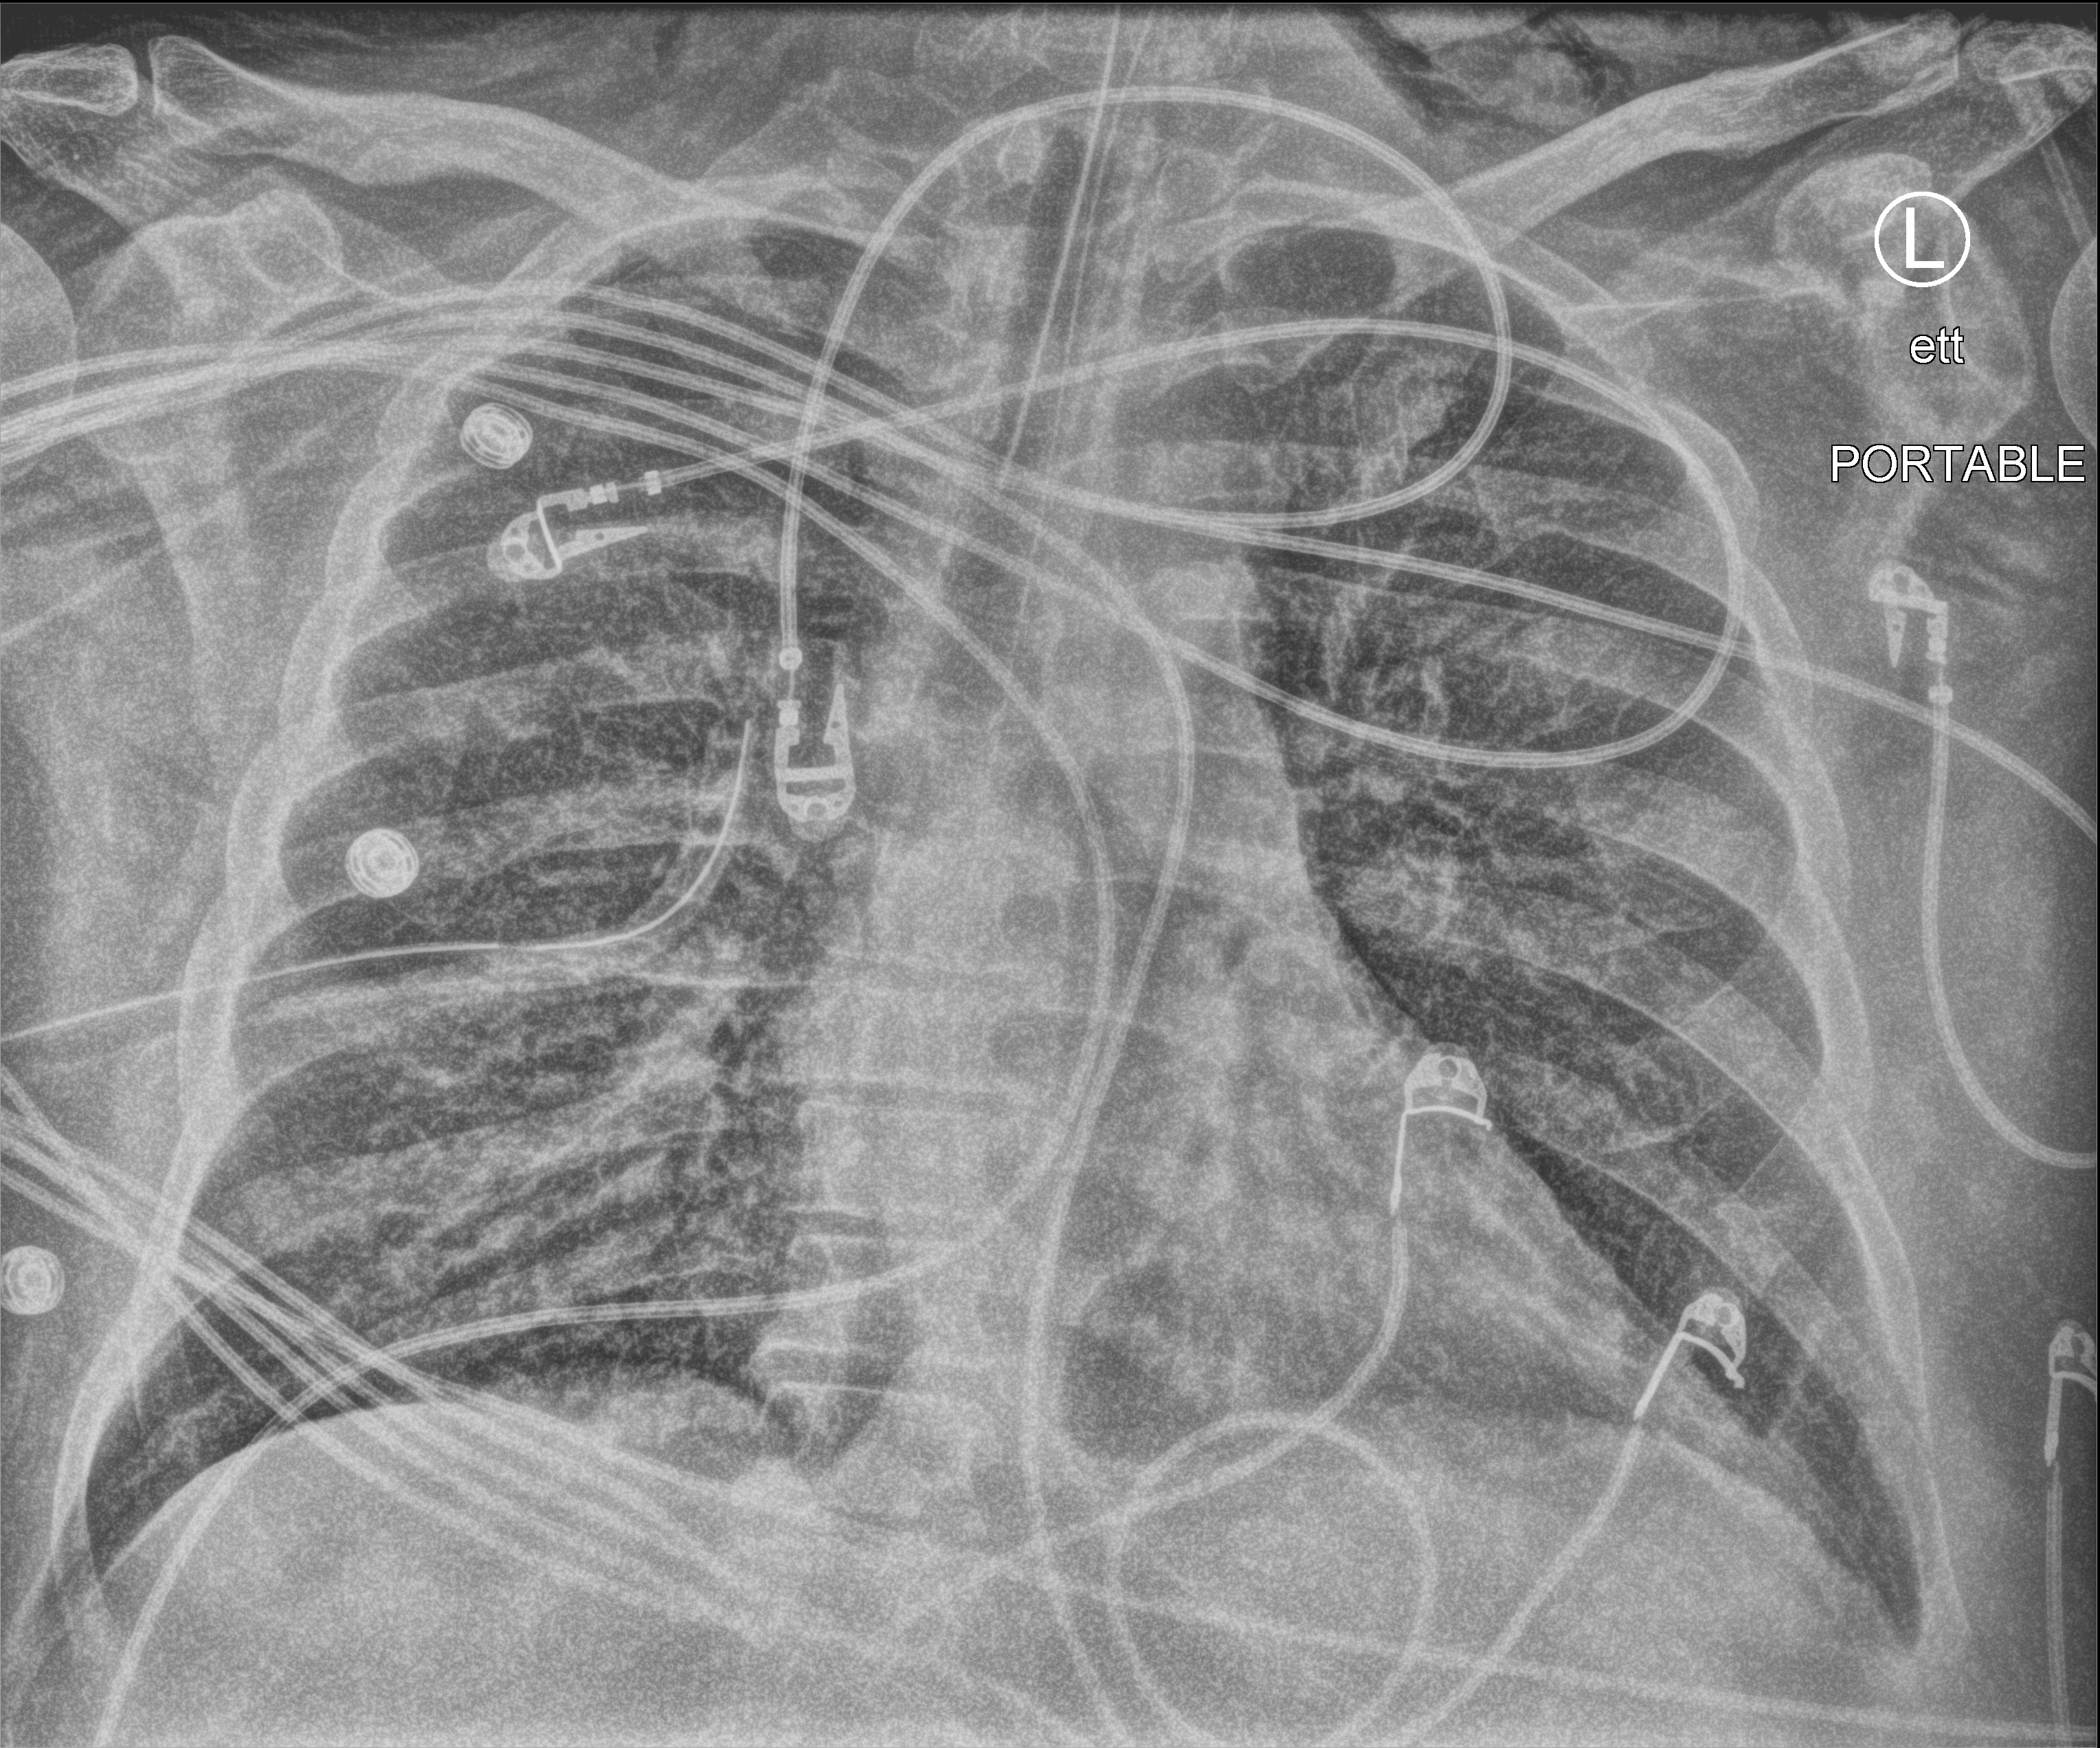
Bedside chest radiograph (computed radiography); anteroposterior (AP) projection. Patient hospitalised with COVID-19, aged 18–59 years.
Hospital-stay facts (about this admission, not read from this image; timing relative to this image not recorded): length of hospital stay: 26 days.